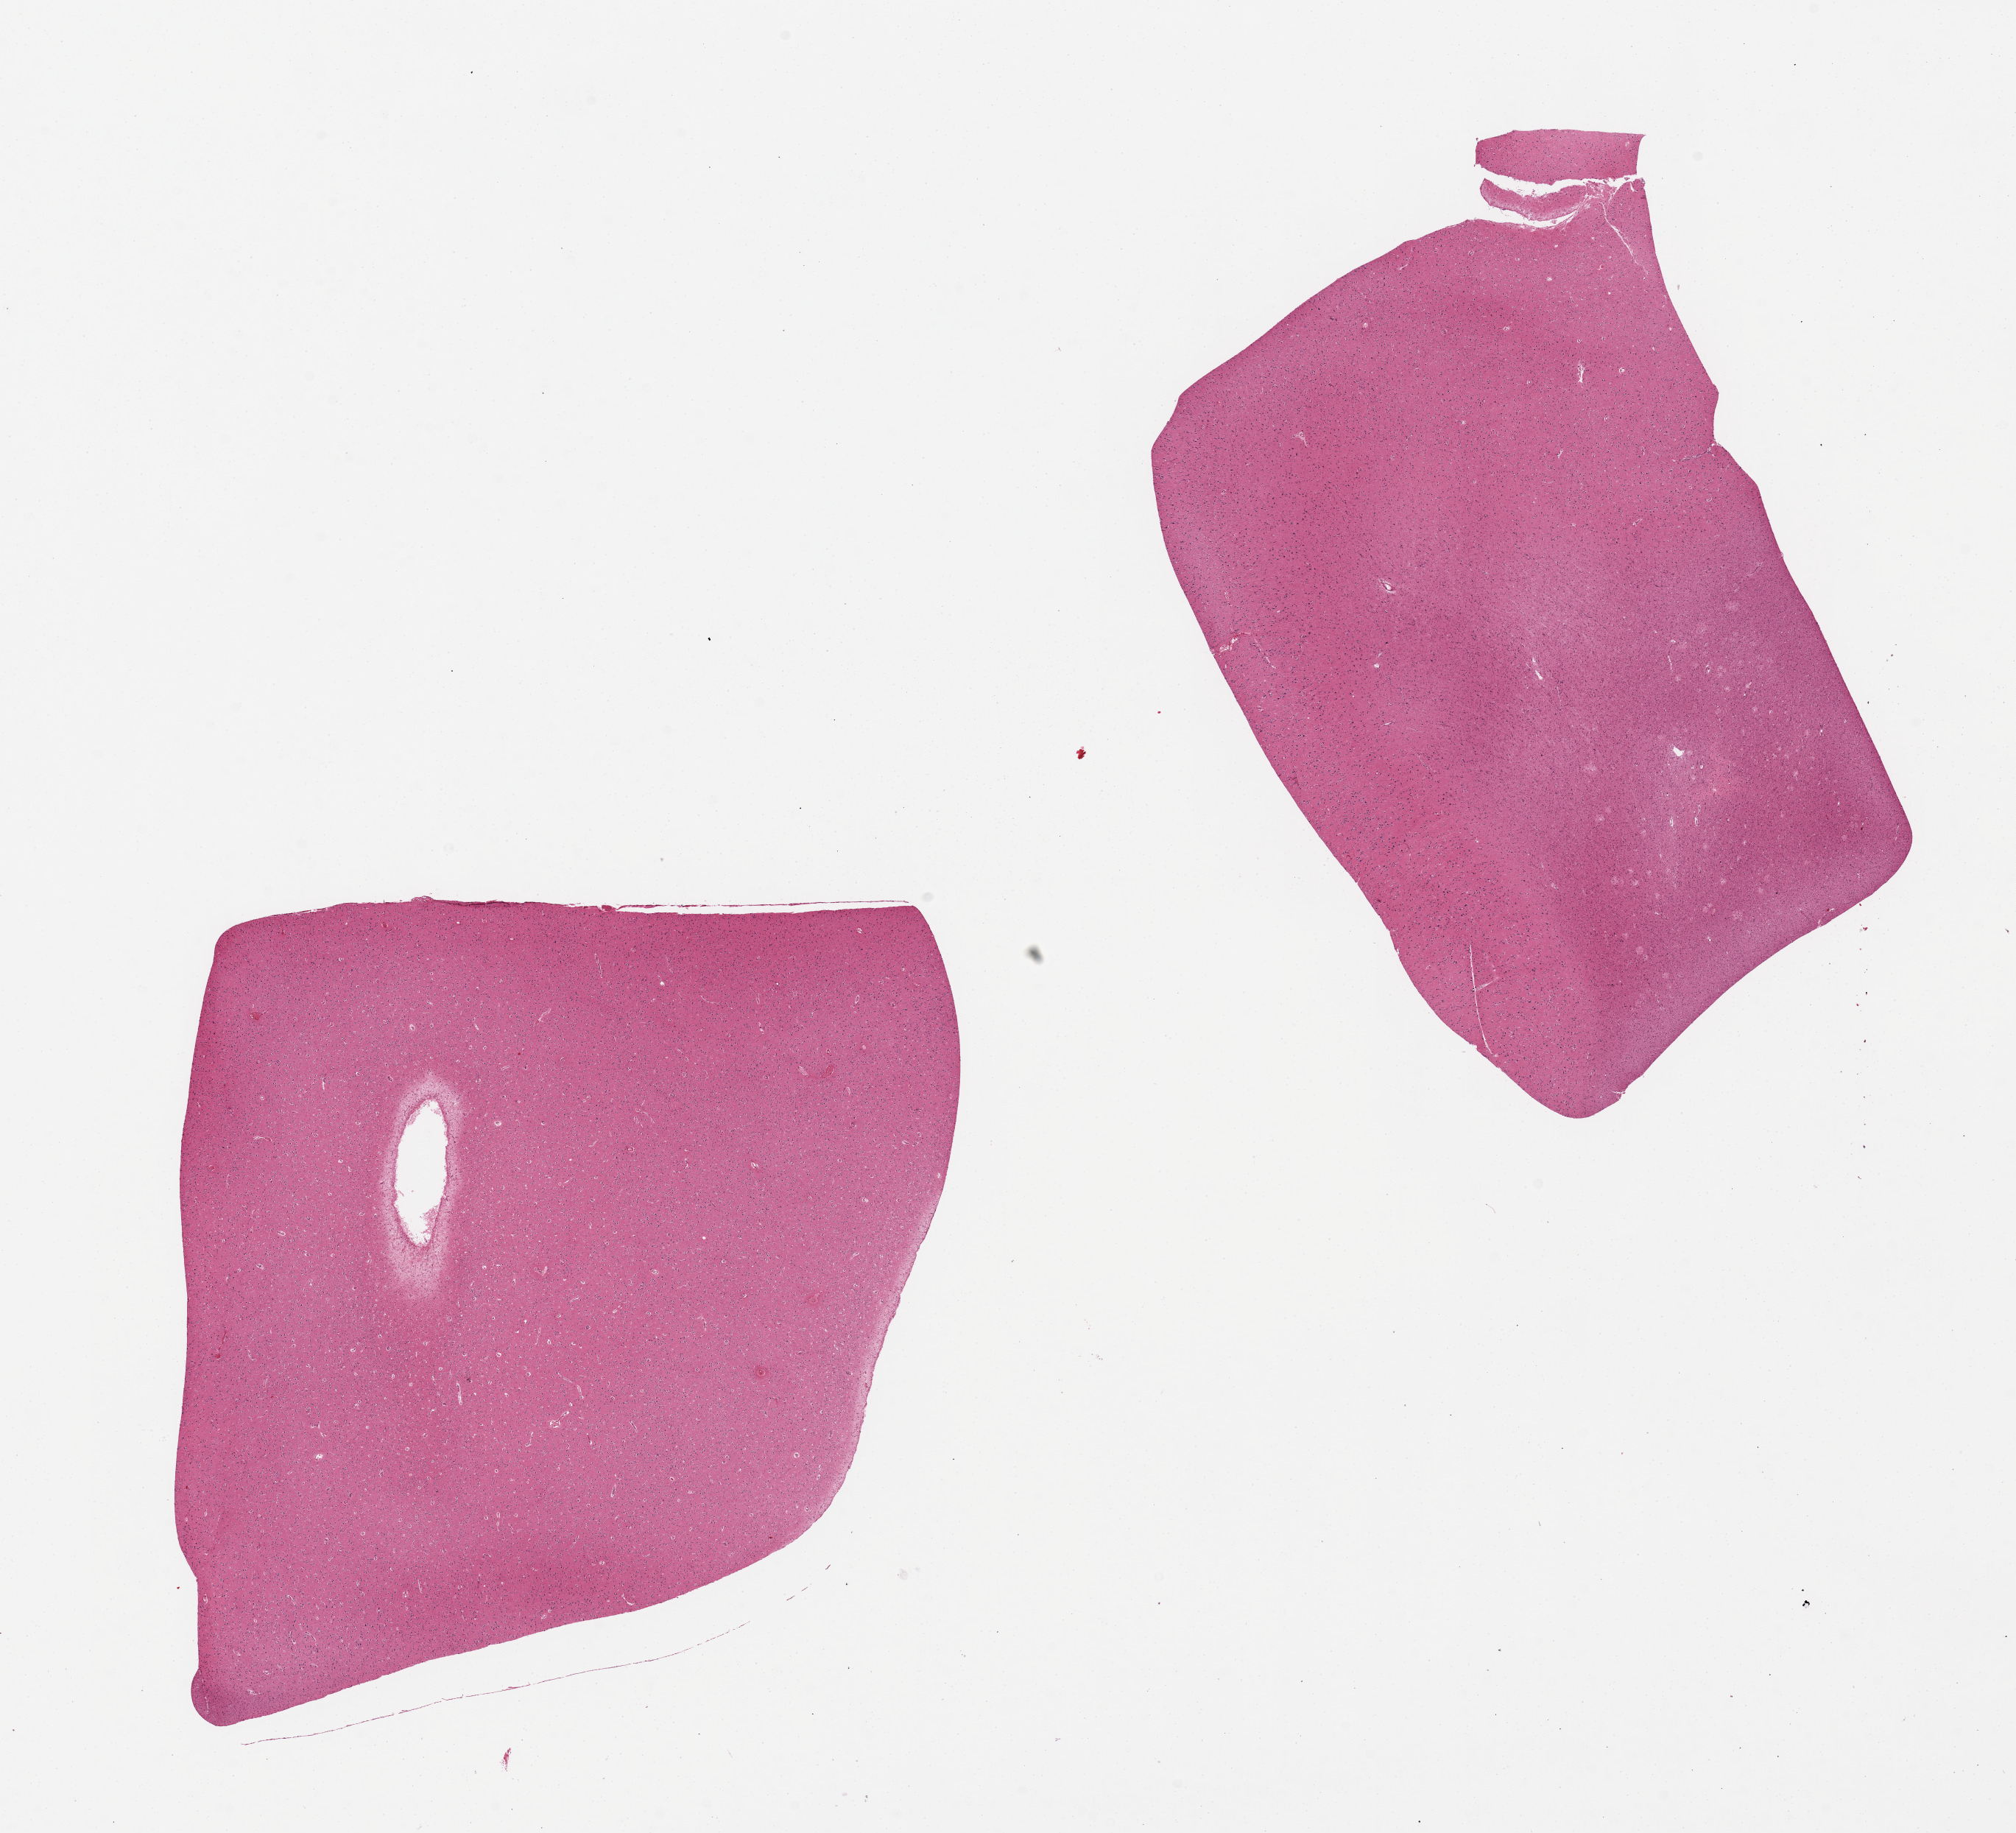
Whole-slide image, H&E stain, shown as a low-resolution overview of the whole scanned area (about 21.7 x 19.7 mm, slide scanned at 20x). PAXgene-fixed paraffin-embedded (PFPE) section. Section of cerebral cortex (target tissue). Tissue donor sample. Female donor.
Reviewer comment on this tissue sample: 2 pieces.